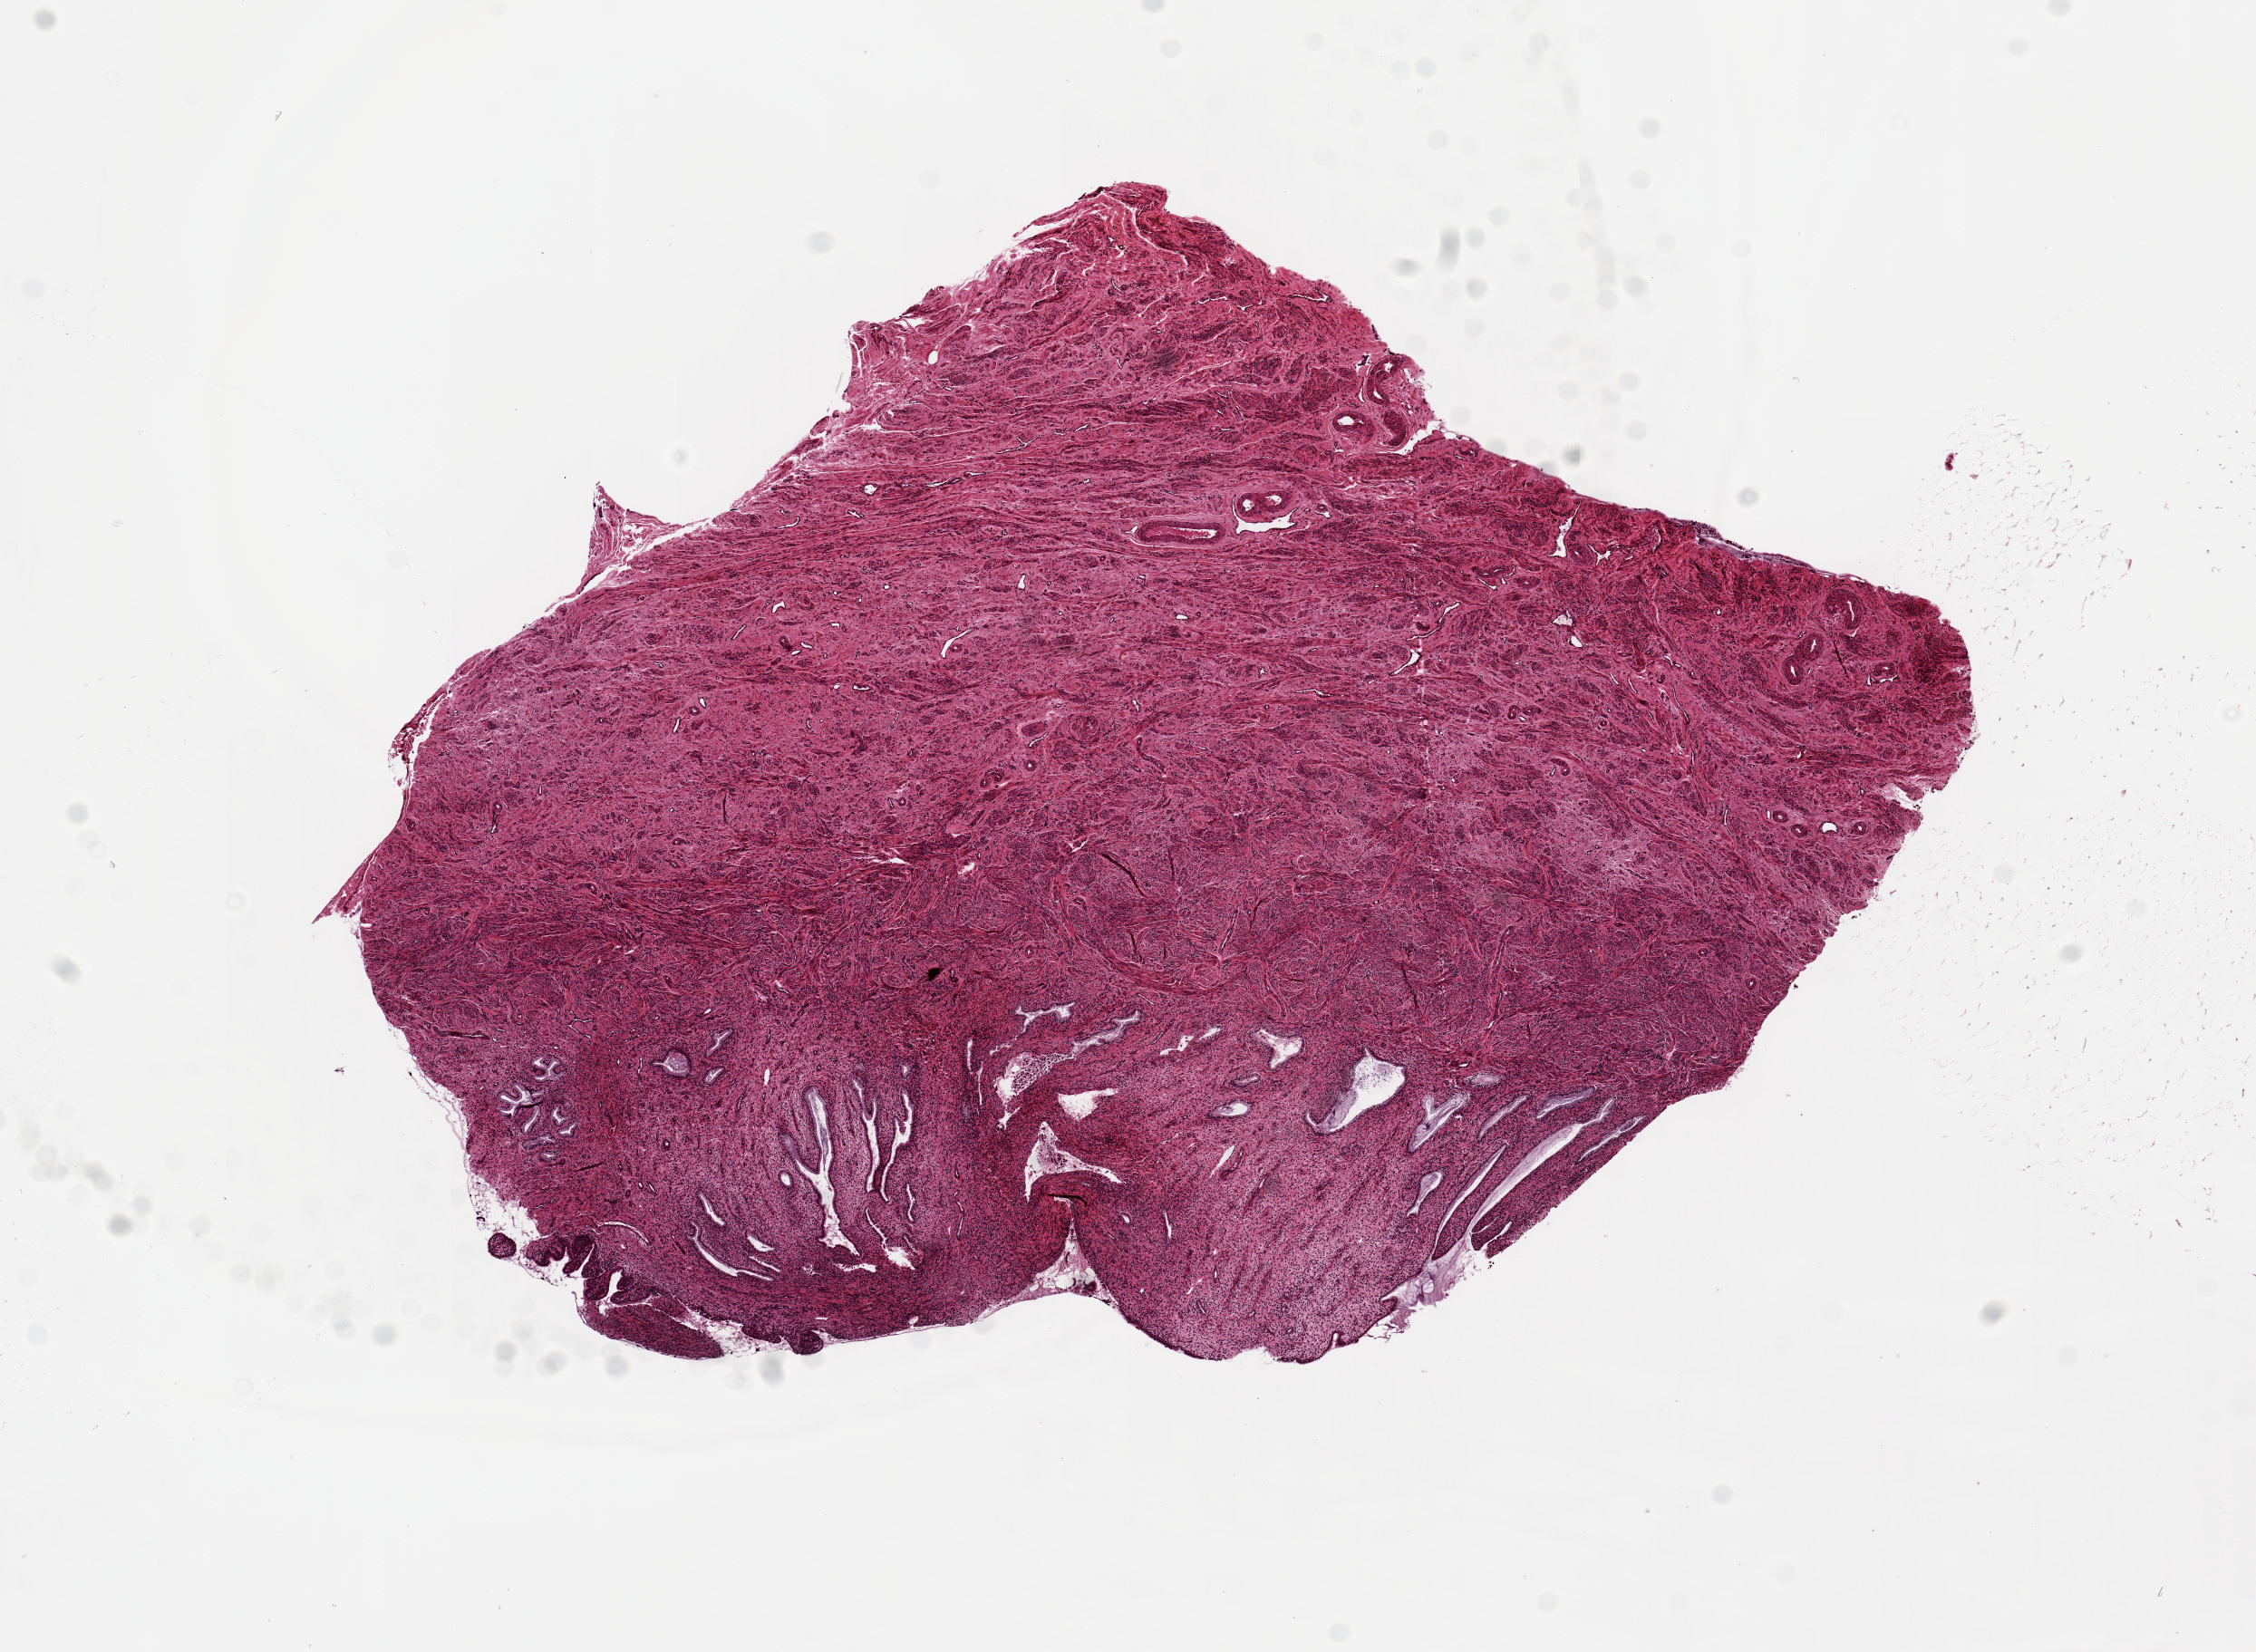
Whole-slide image, haematoxylin and eosin stain — a low-resolution overview of the entire scanned area, about 9.8 x 7.2 mm (from a 20x scan). PAXgene-fixed, paraffin-embedded tissue. Target tissue: endocervix. Tissue donor sample. Female donor.
- pathologist's review note for this sample: ~6x5mm. No squamous mucosa. A 5x1.3mm area of endocervical glands on one edge